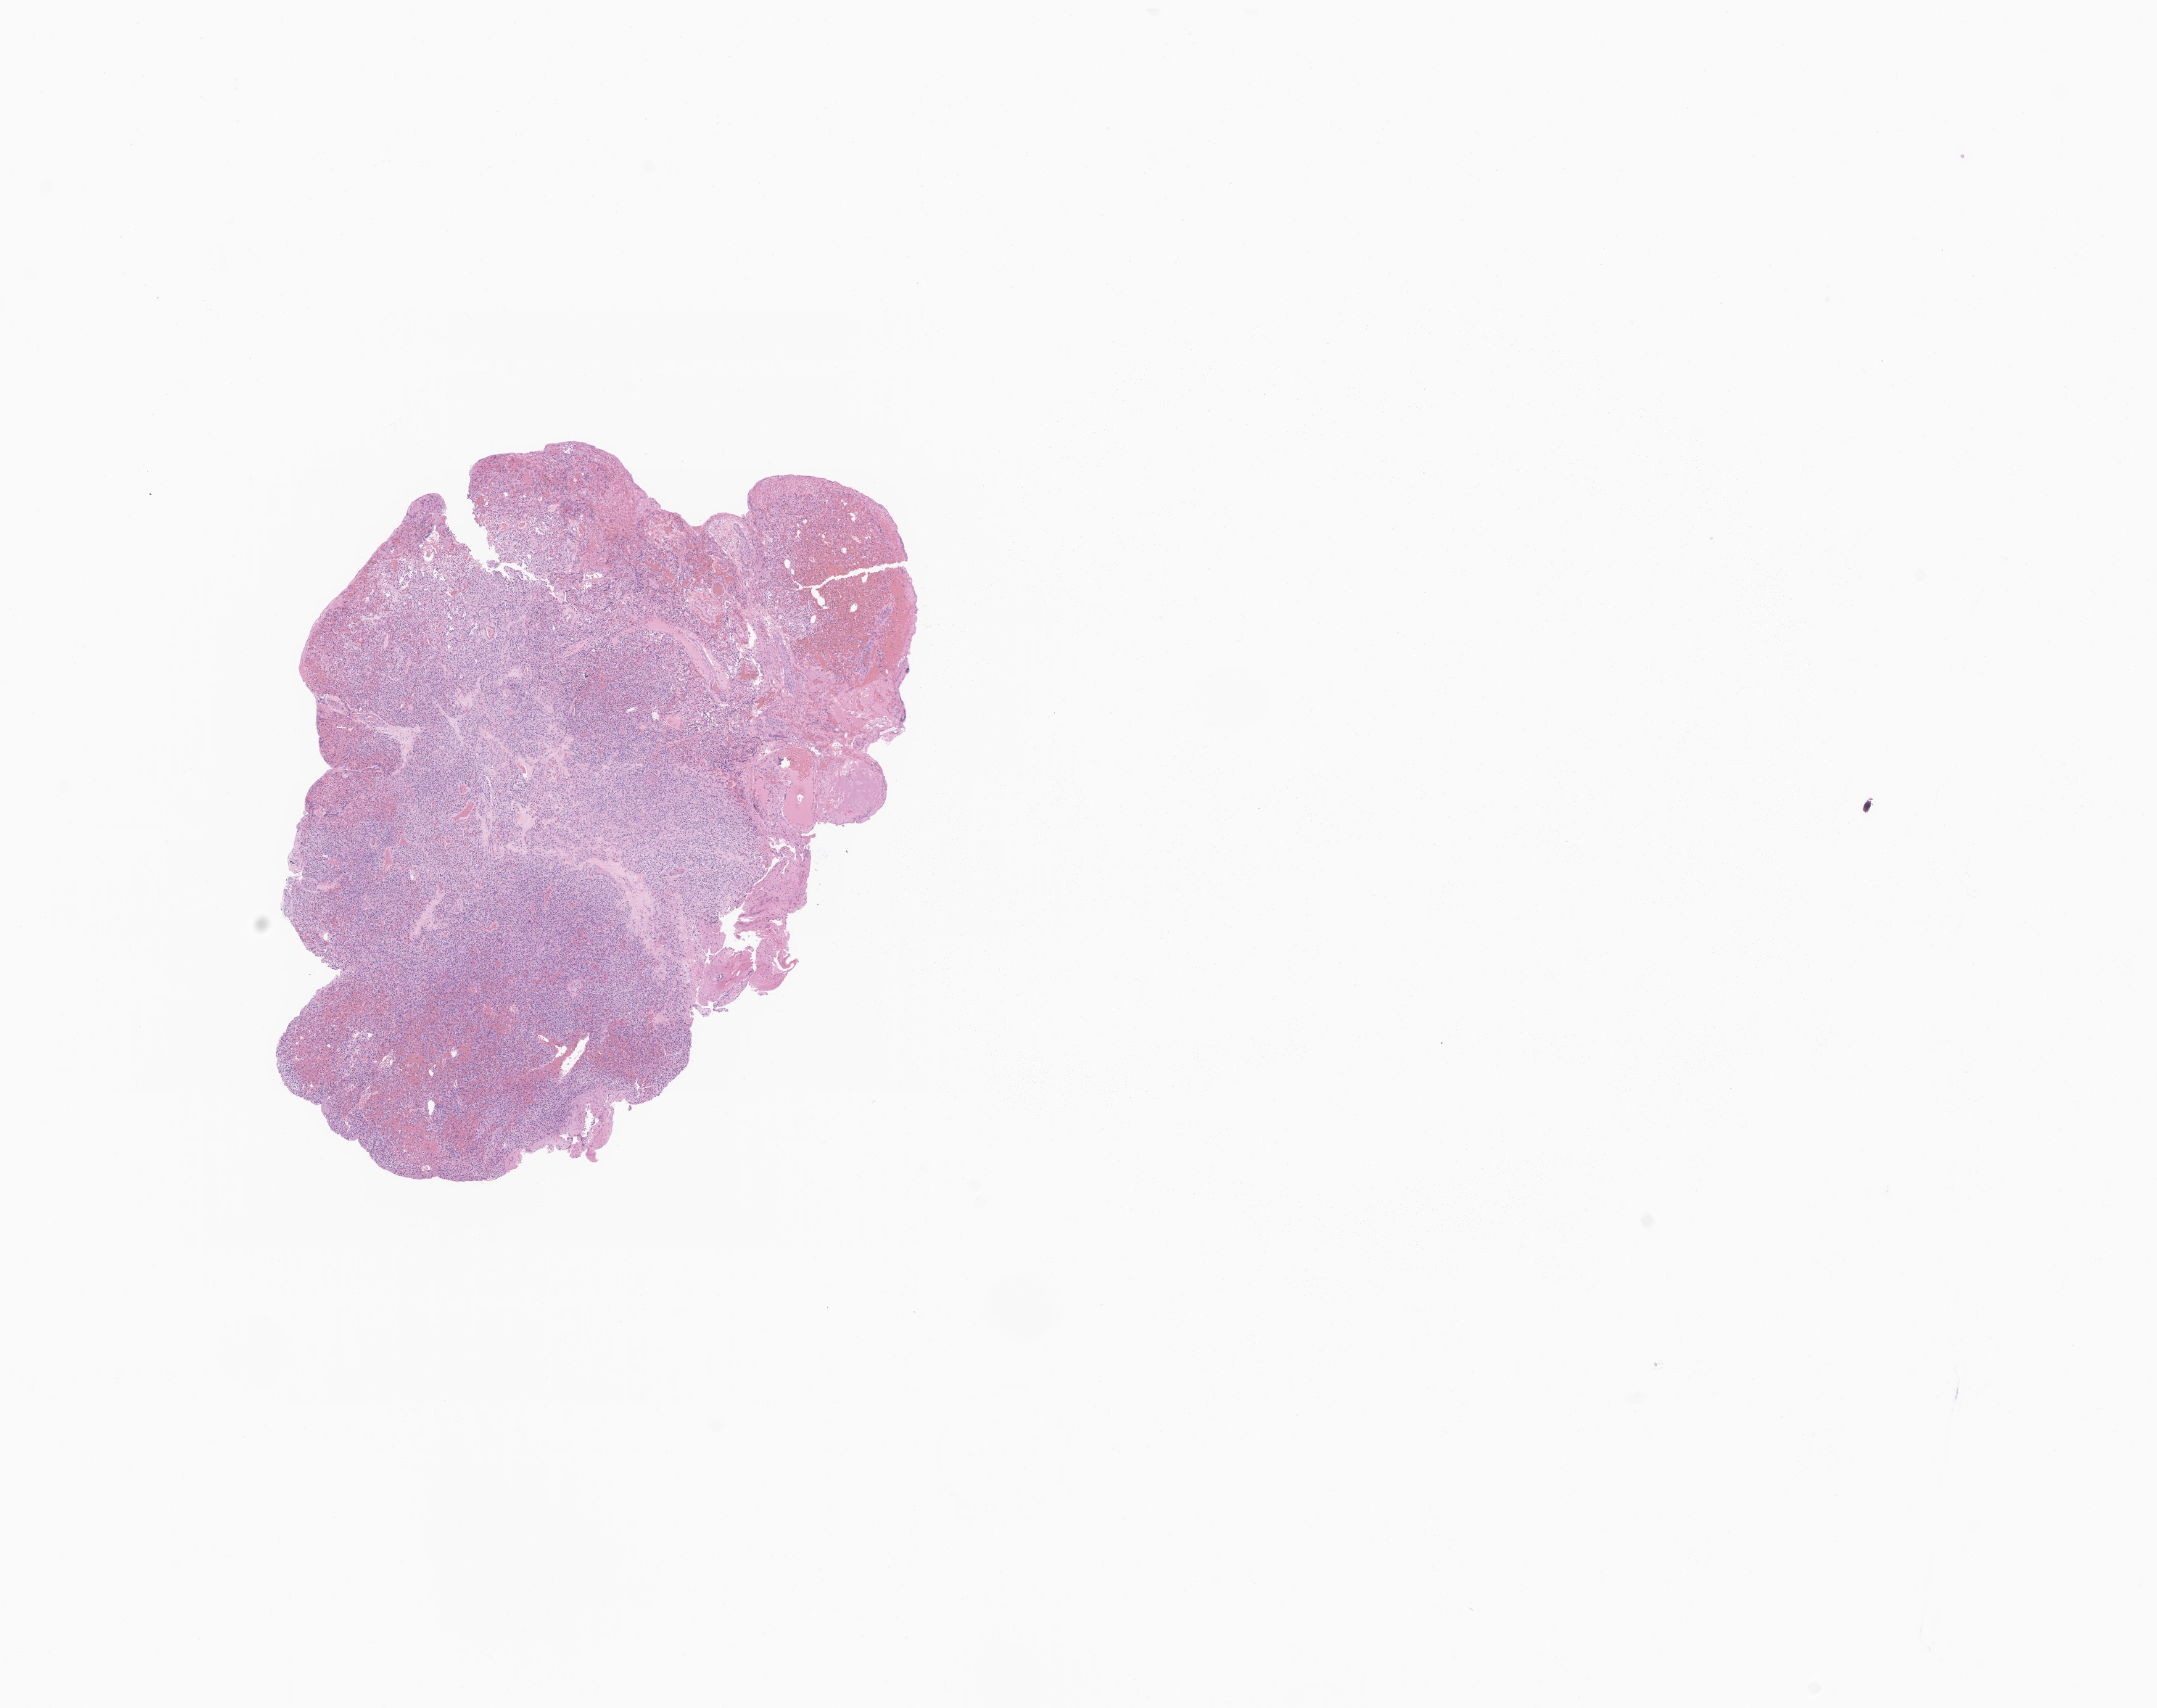
Digitized H&E-stained section of tumor tissue from the brain, a low-resolution overview of the entire scanned area, about 14.7 x 11.7 mm. FFPE section. Female patient, age 110 months (9 years 2 months).
• diagnosis (ICD-O-3 morphology term): Hemangioblastoma